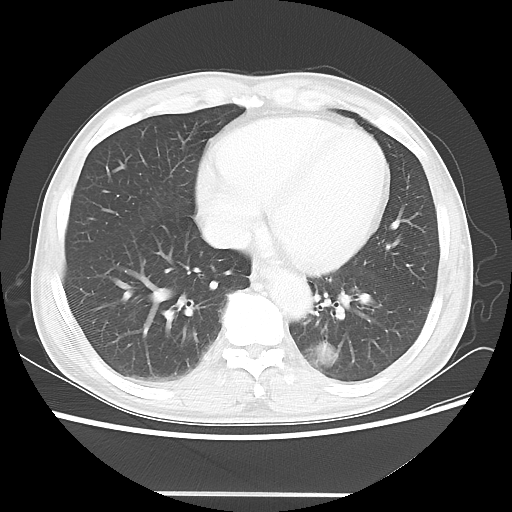
Chest CT, one axial slice; slice 19 of 60 in the series (ordered by position); reconstruction kernel LUNG; 100 kVp; lung window (W 1500 / L -600 HU); 5 mm slice thickness; 512 × 512 image matrix, field of view 360 × 360 mm. Patient: male, 55 years. Case-level facts recorded for this patient, not image findings: clinical TNM (as recorded): T1c N3 M0.
Annotated regions visible in this slice (rectangle marked by the reading radiologist):
- lung tumour (recorded histology: small cell carcinoma): bounding box <297,333,347,374> (left, top, right, bottom; pixels)